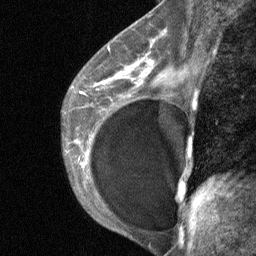
Breast MRI (dynamic contrast-enhanced), one sagittal slice. Slice 41 of 64 in the series (ordered by position). Dynamic contrast-enhanced study with each time point stored as its own series, time point 2 of 3 at this slice position (early post-contrast, ordered by acquisition time). 1.5 T. TE 4.8 ms, TR 27 ms. 2 mm slice thickness. 256 × 256 image matrix. Female patient, age 35 years. From the clinical record (not read from this slice): setting: breast cancer imaged before/during neoadjuvant chemotherapy; receptor status: HR-positive, HER2-negative.
Outlined on this slice (semi-automatic segmentation, software-assisted and operator-edited):
- analysis volume of interest (the breast-tissue region the enhancement analysis was run in; not a lesion): box from (x=74, y=58) to (x=171, y=171) px
- tumour enhancement mask (voxels above the 90 % enhancement threshold inside the analysis volume of interest): (x=80, y=82)–(x=104, y=94)